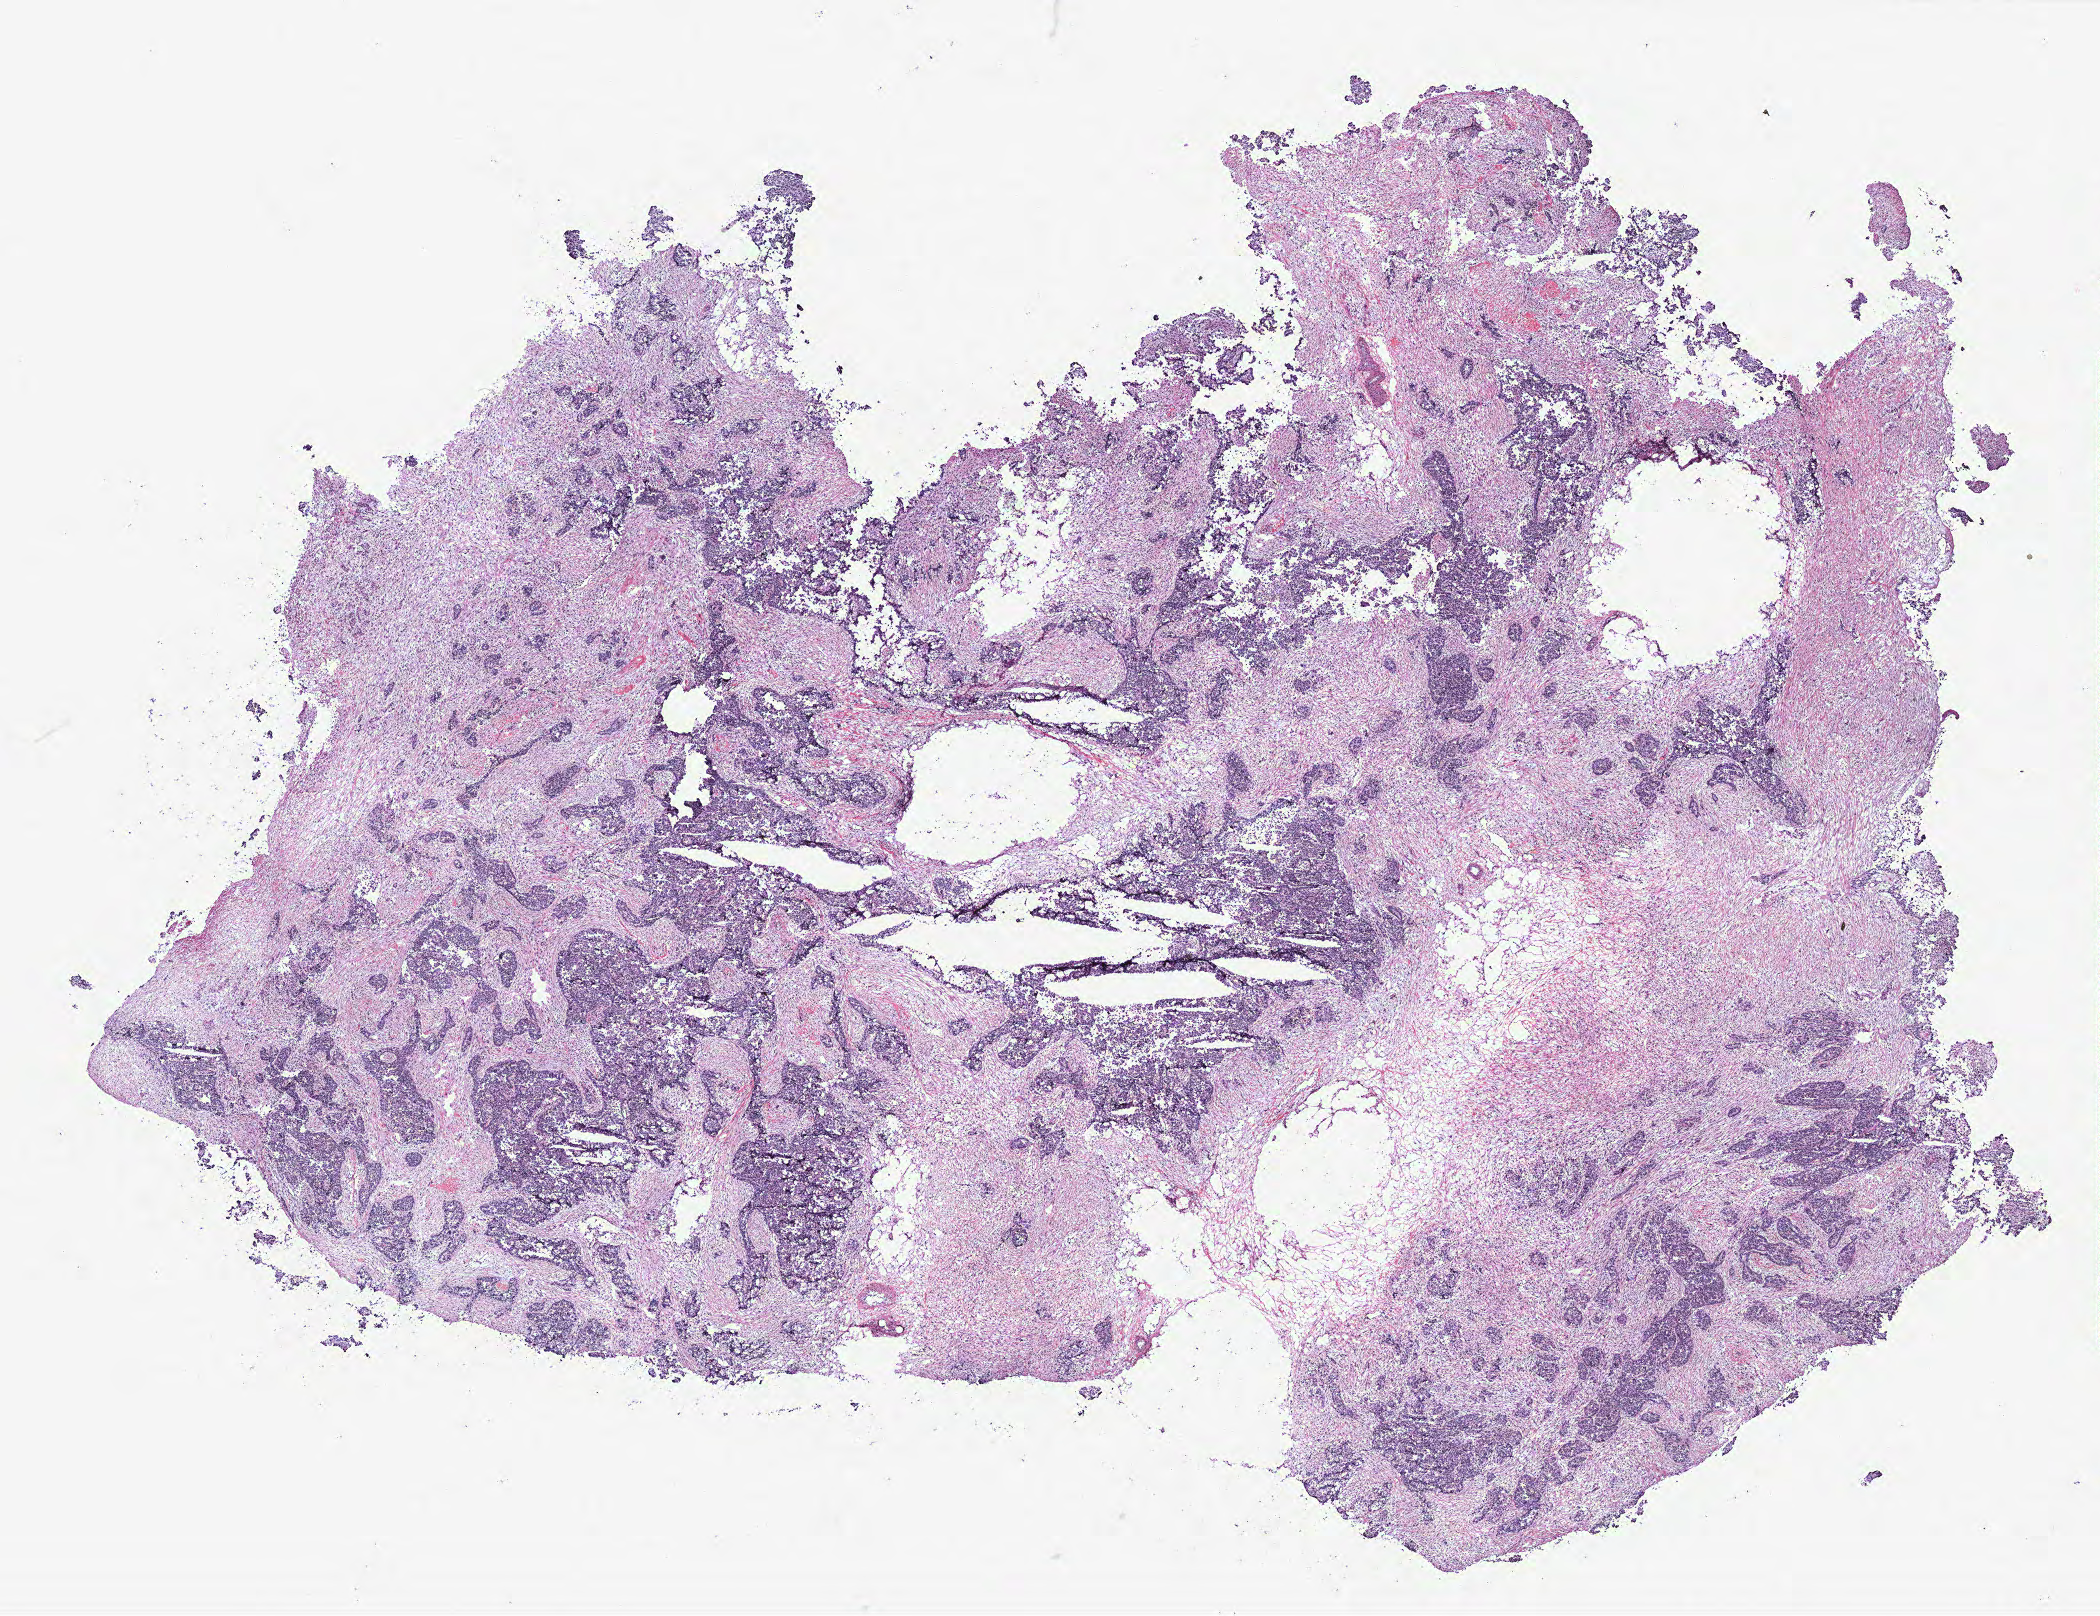
Whole-slide histology image, H&E-stained — low-resolution overview of the scanned area, about 16.8 x 12.9 mm (acquisition: 40x scan), ovary, tumour tissue. Female, 59 y/o.
Primary tumour site (as recorded): fallopian tube. Histologic diagnosis: Serous adenocarcinoma, NOS.